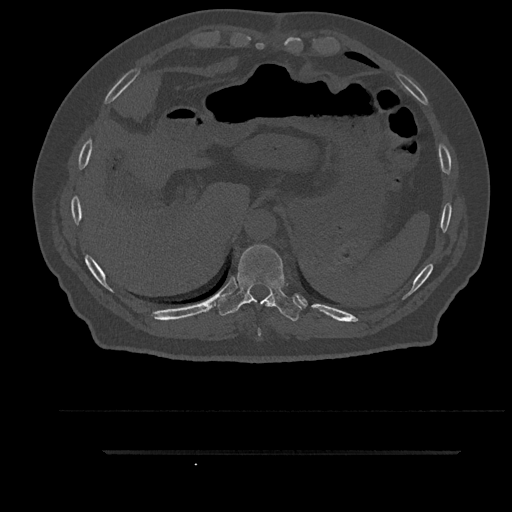
CT including the spine, one axial slice; slice 379 of 797 in the series (ordered by position); bone window (W 1800 / L 400 HU); 0.5 mm slice thickness; 512 × 512 image matrix. Male patient, age 63 years. Case-level facts recorded for this patient, not image findings: primary cancer: renal.
Annotated regions visible in this slice (semi-automatically segmented with operator editing):
- T10 vertebra: bounding box <218,245,303,321> (left, top, right, bottom; pixels)
- T9 vertebra: <258,302,268,336>